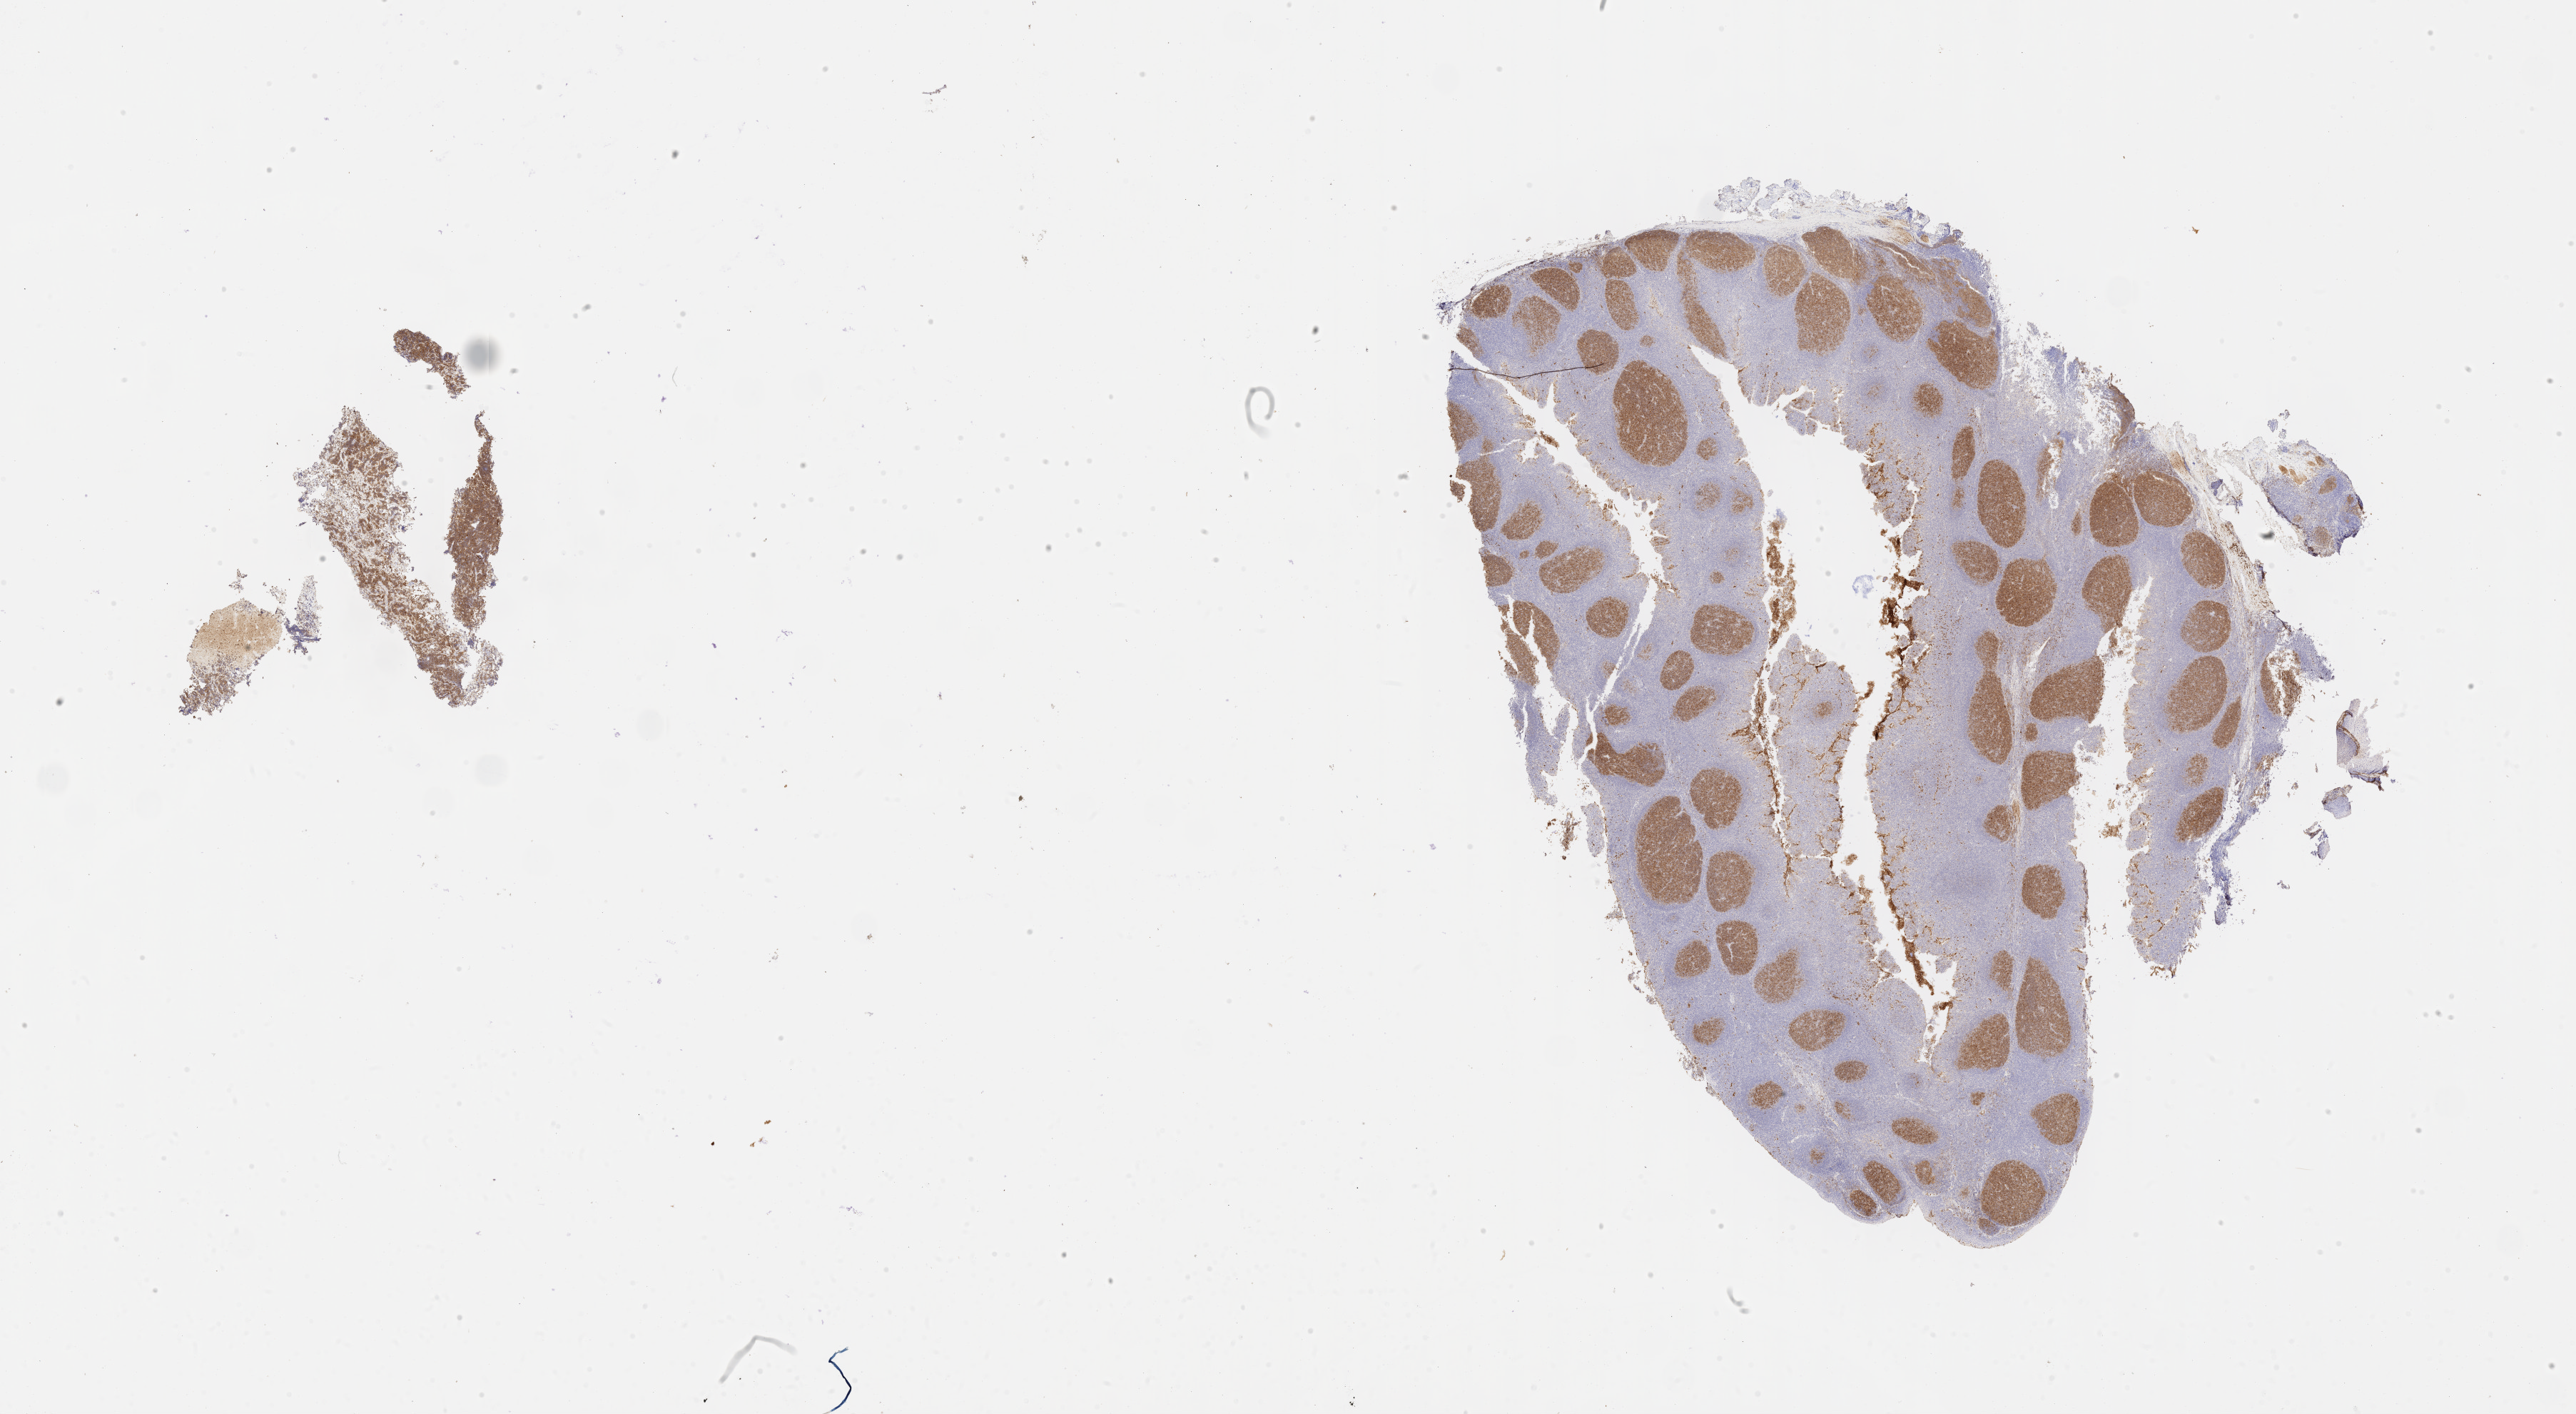
Whole-slide image, immunohistochemical stain for CD10 — low-resolution overview of the scanned area, about 29.2 x 16.0 mm, specimen: tumor tissue, anatomic site: pelvis. Female patient; age at initial diagnosis 7 years.
Histologic diagnosis: Burkitt lymphoma, NOS.